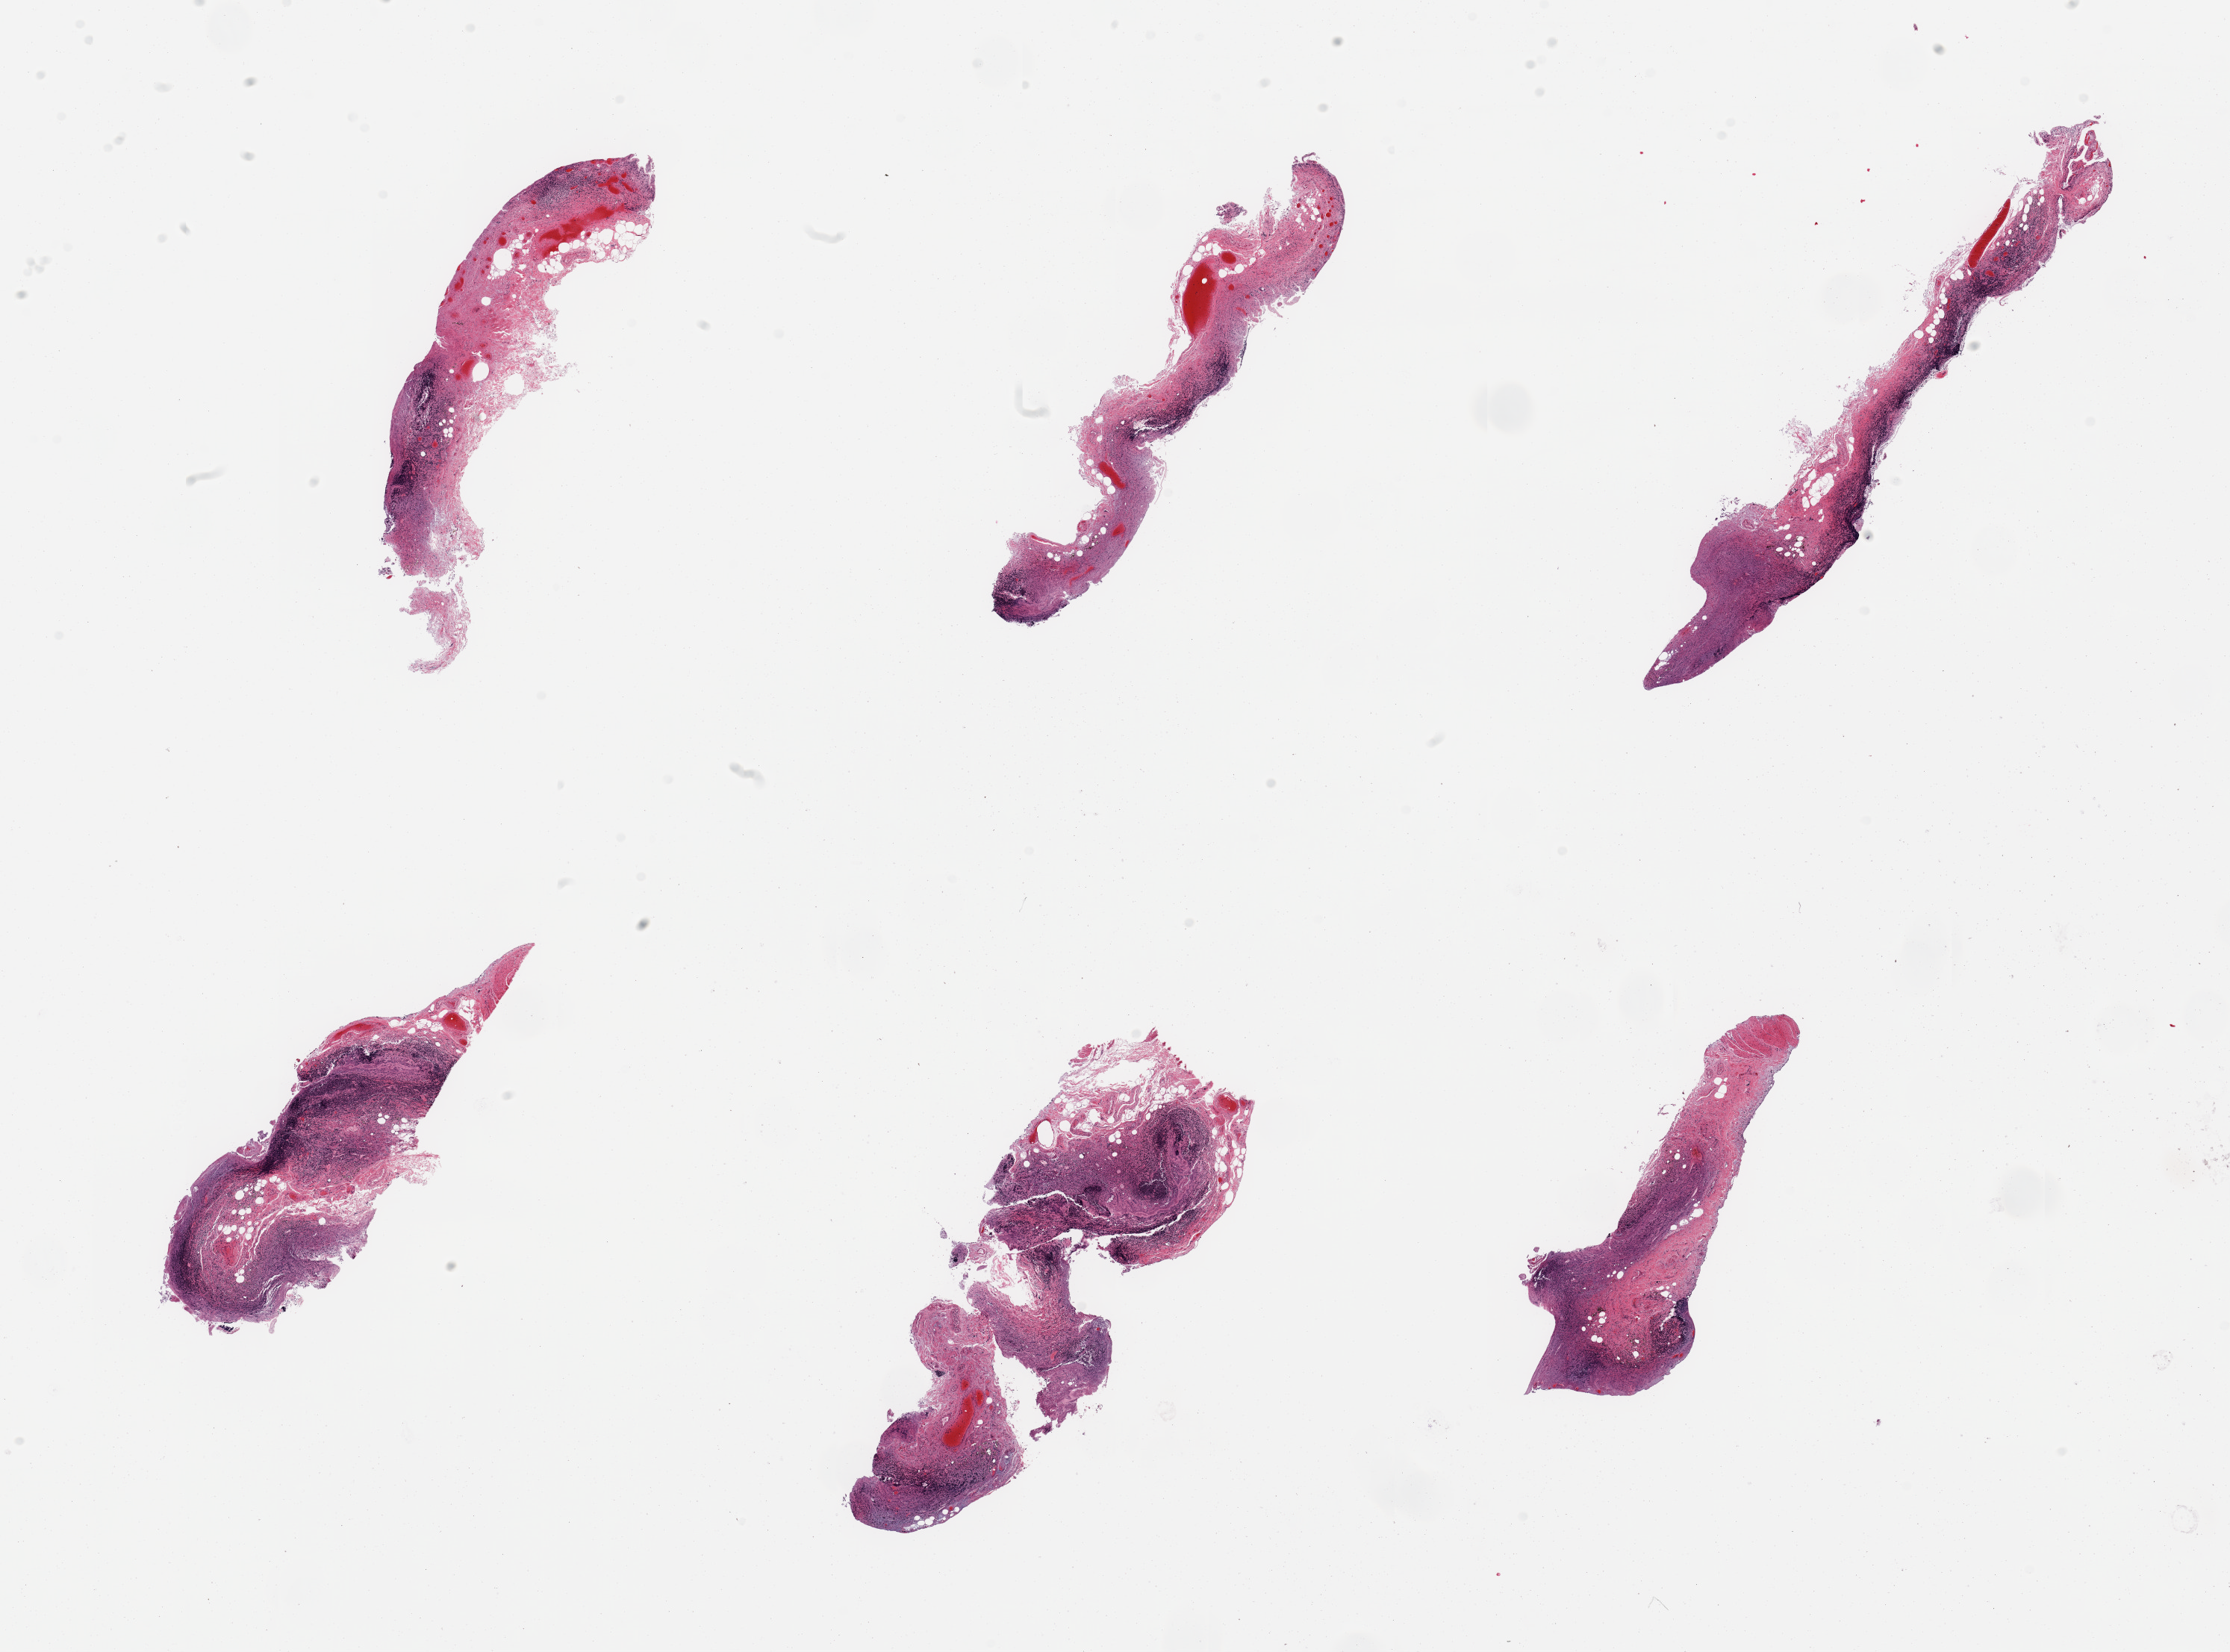
Digitized hematoxylin and eosin (H&E)-stained section, brightfield, whole scanned area (about 23.6 x 17.5 mm, slide scanned at 20x) shown as a low-resolution overview, PAXgene-fixed paraffin-embedded (PFPE) section, section of ileum (target tissue), donor tissue sample. Donor: female.
Reviewer comment on this tissue sample: 6 pieces, ~30% target lymphoid aggregates.